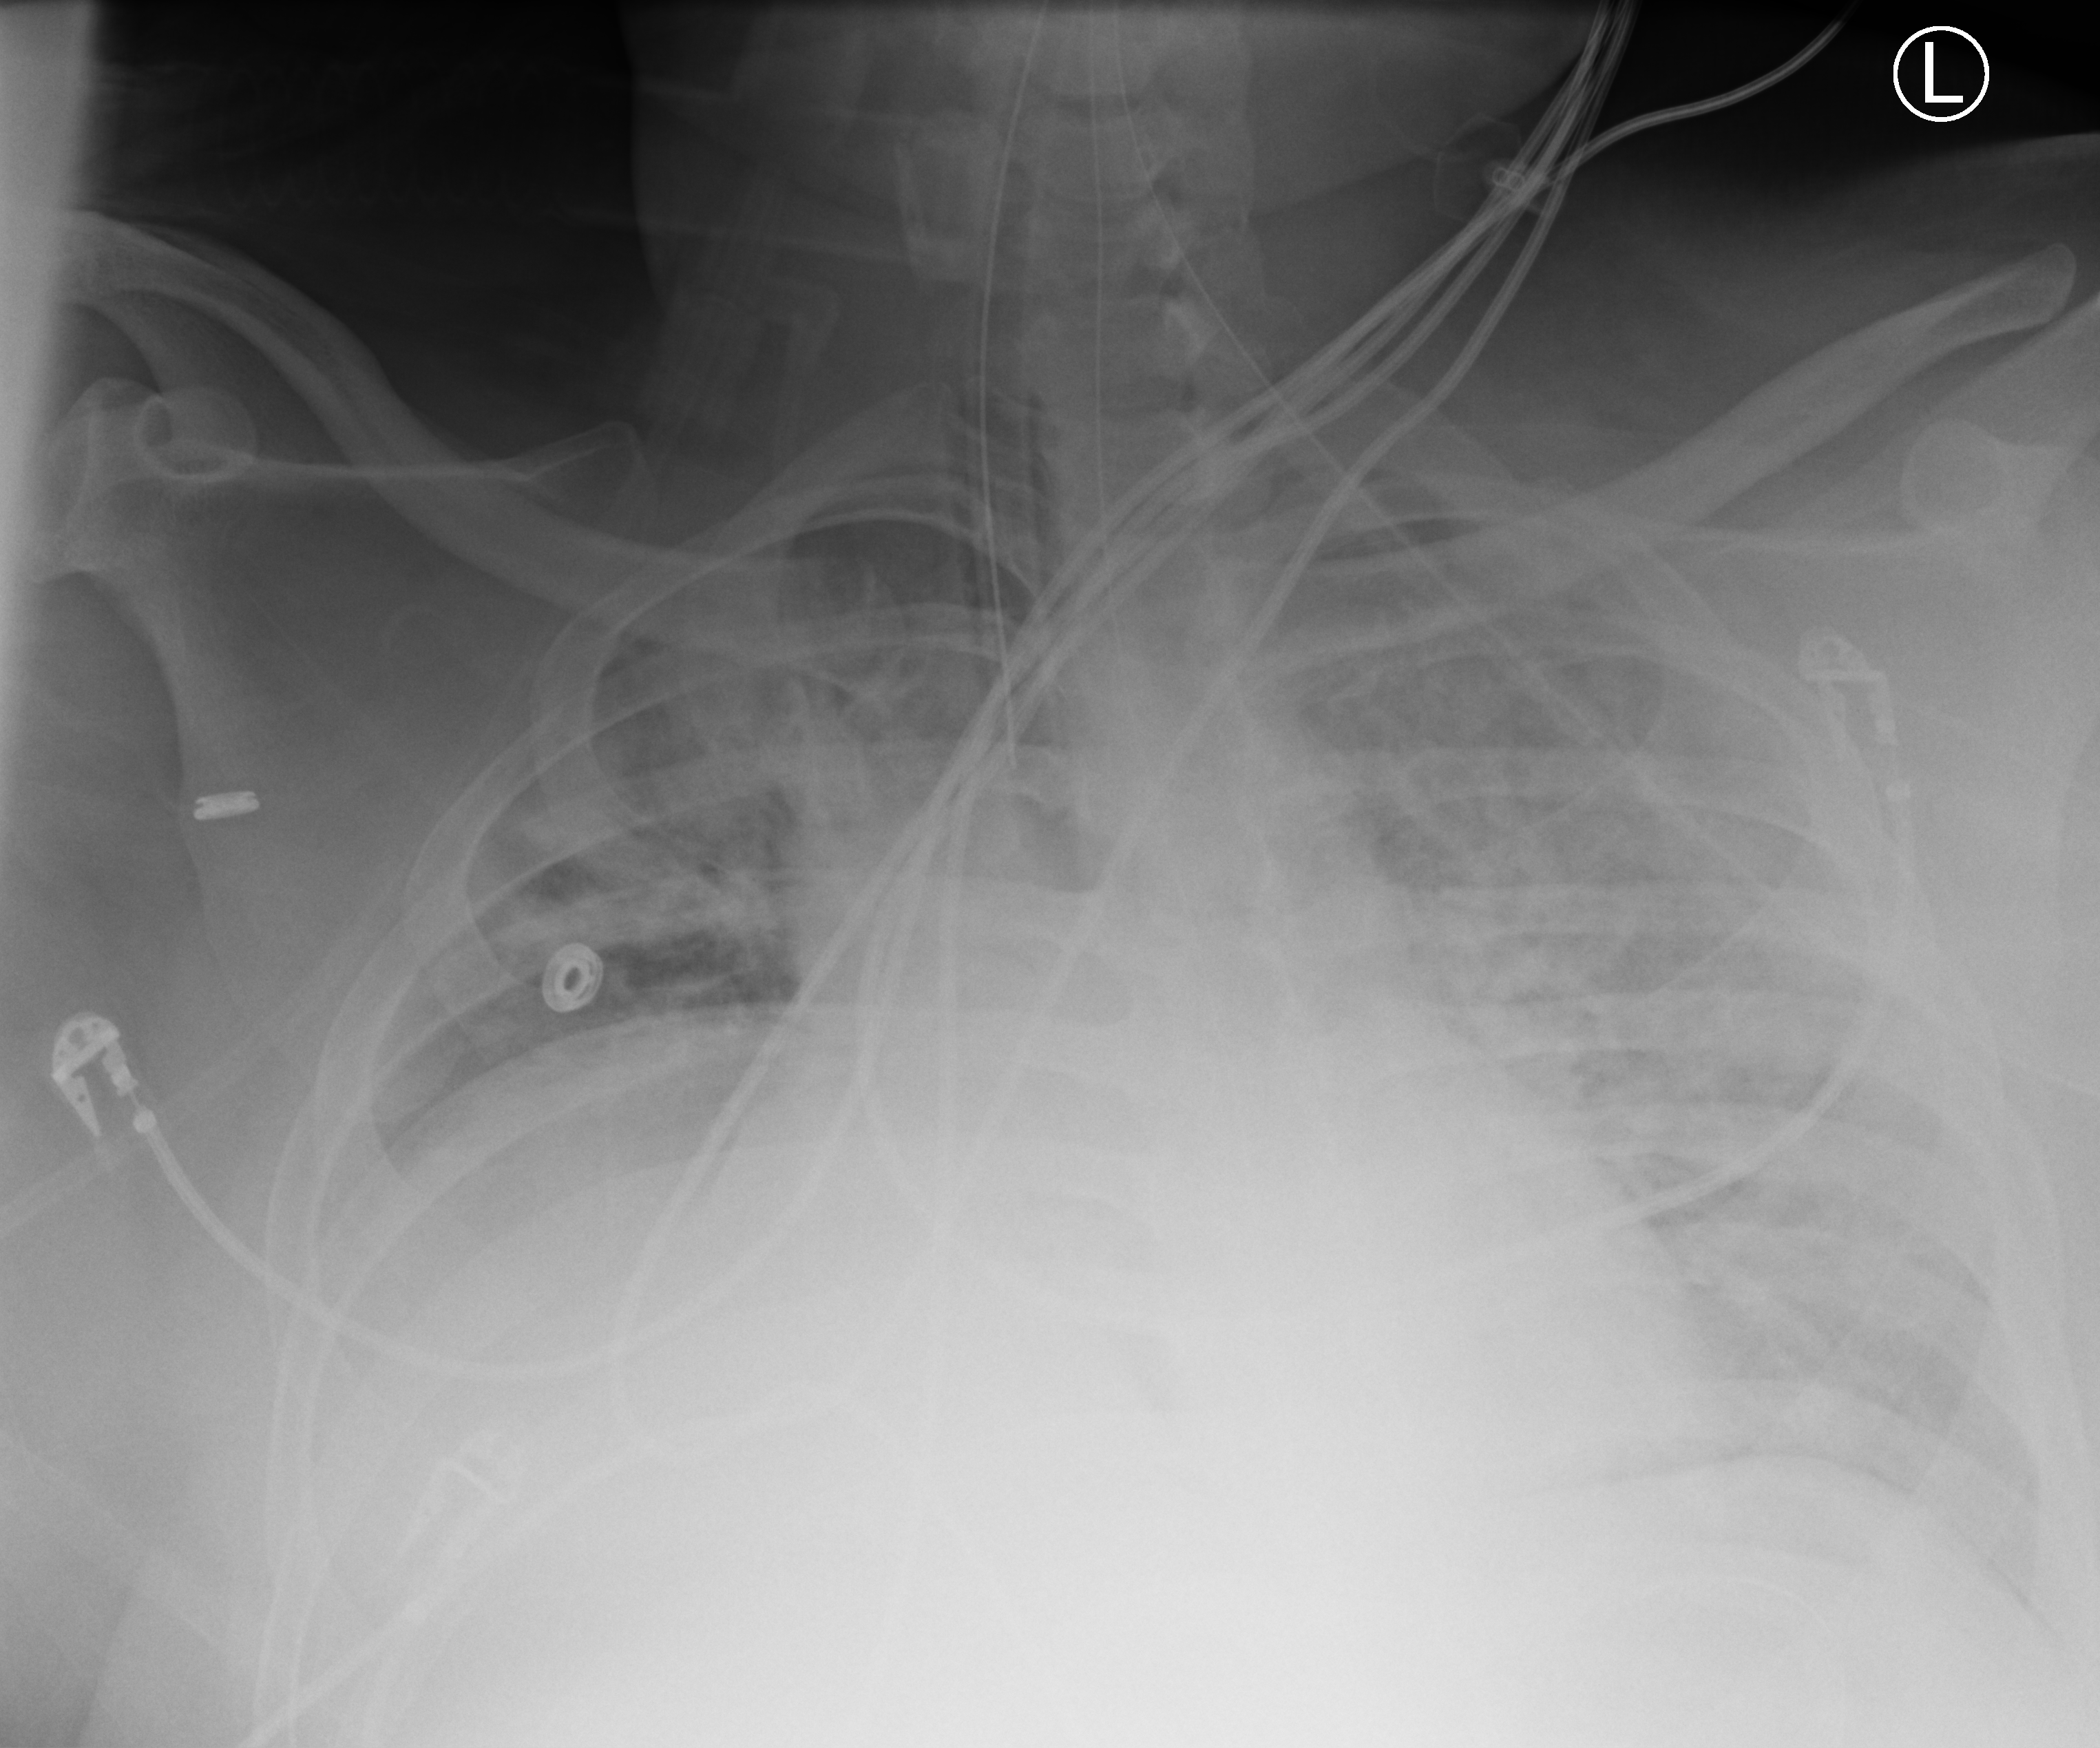
Chest X-ray (portable), anteroposterior (AP) projection. Male patient hospitalised with COVID-19, age 18–59 years.
From the hospital-stay record, not from the radiograph (when in the stay this image was taken is not recorded):
- length of hospital stay: 69 days